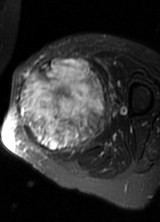
MRI of an extremity soft-tissue mass, one axial slice; position 33 of 69 along the scan axis; T2-weighted fat-saturated; MR volume resampled by the dataset authors to the PET/CT grid (not the native acquisition matrix); 160 × 222 image matrix, field of view 156 × 217 mm. Female patient. Case-level facts recorded for this patient, not image findings: histological type: pleomorphic leiomyosarcoma; grade: high; site of the primary tumour: left thigh.
Annotated regions visible in this slice (expert contour drawn on MRI and transferred to this co-registered scan by the dataset authors):
- gross tumour volume including surrounding oedema: bounding box (x1, y1, x2, y2) in pixels: (16, 57, 110, 156)
- gross tumour volume (mass): (16, 59, 106, 153)